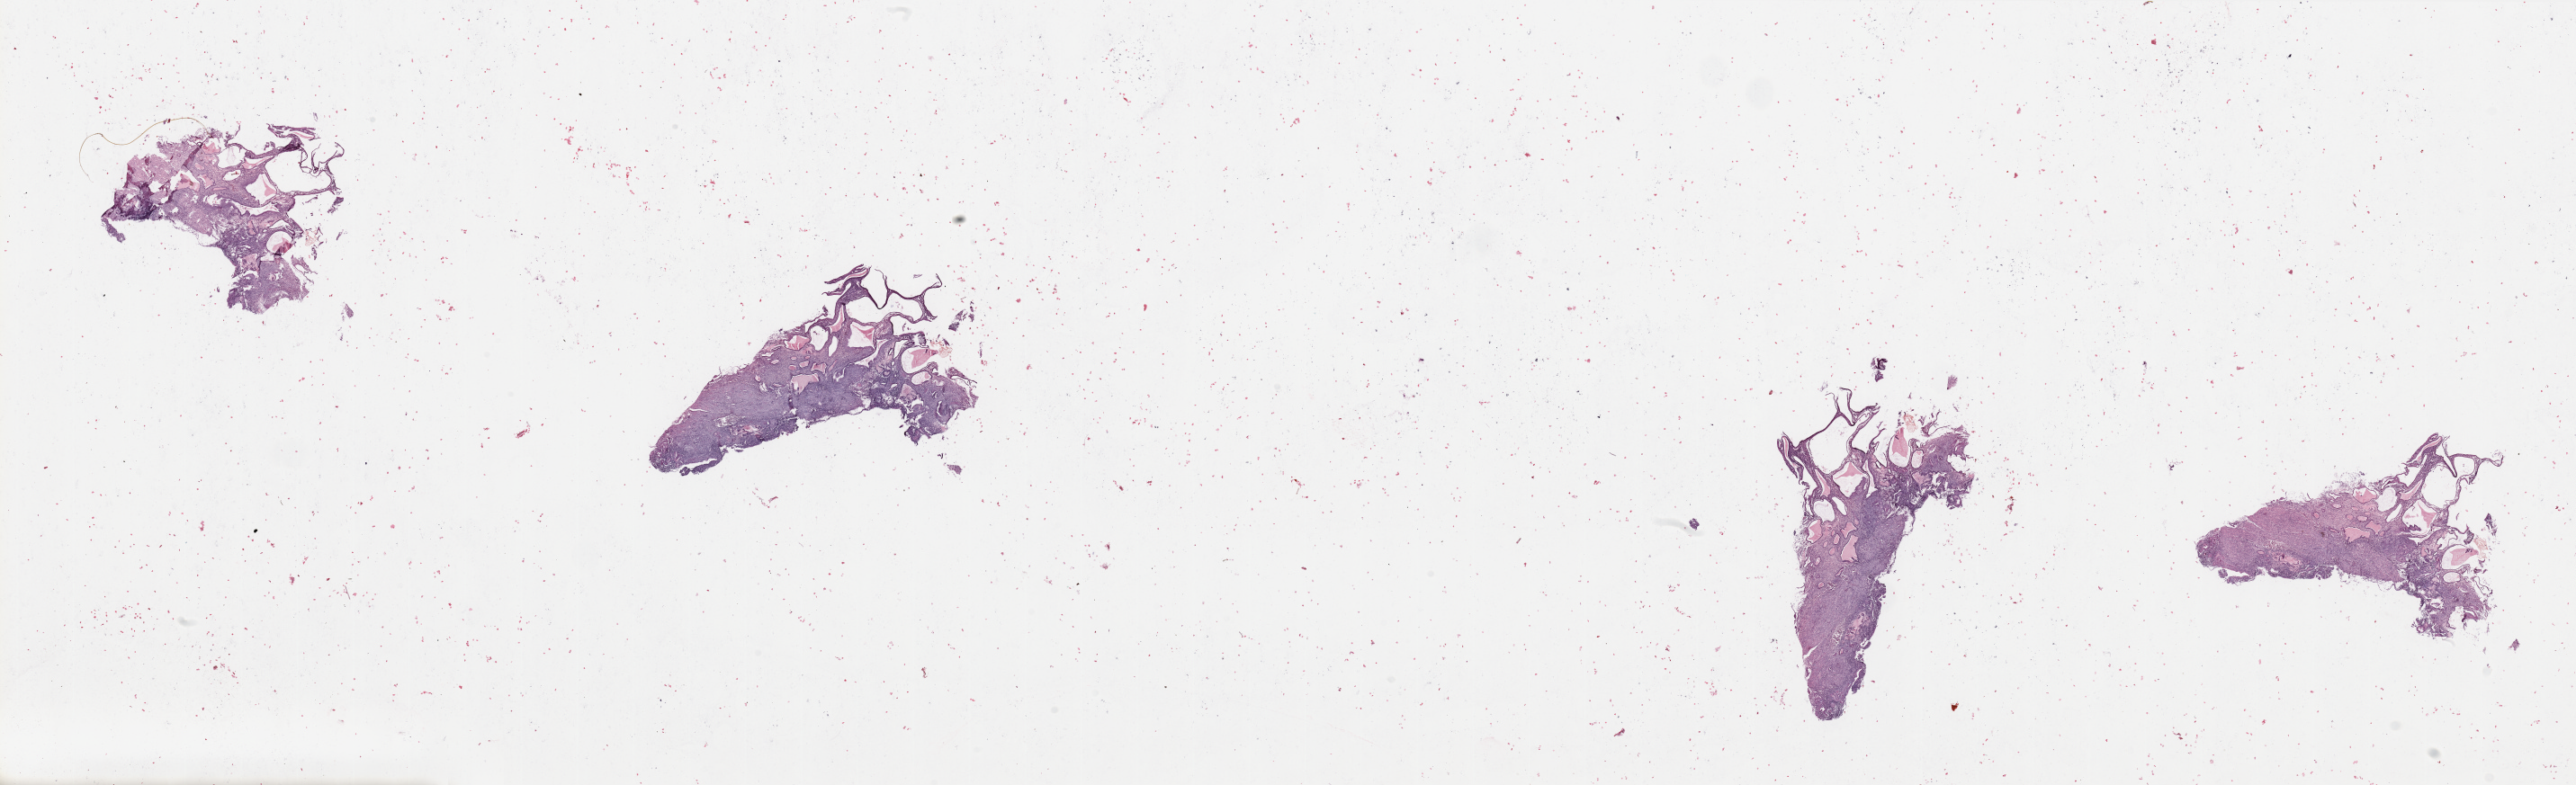
Digitized Hematoxylin and eosin (H&E) stained tissue section (whole slide) — shown as a low-resolution overview of the whole scanned area (about 45.3 x 13.8 mm, slide scanned at 20x); uterus, normal (non-tumour) tissue. Patient: female, age 77 years.
This section: normal (non-tumour) tissue from the same patient. Patient diagnosis: Endometrioid adenocarcinoma, NOS.